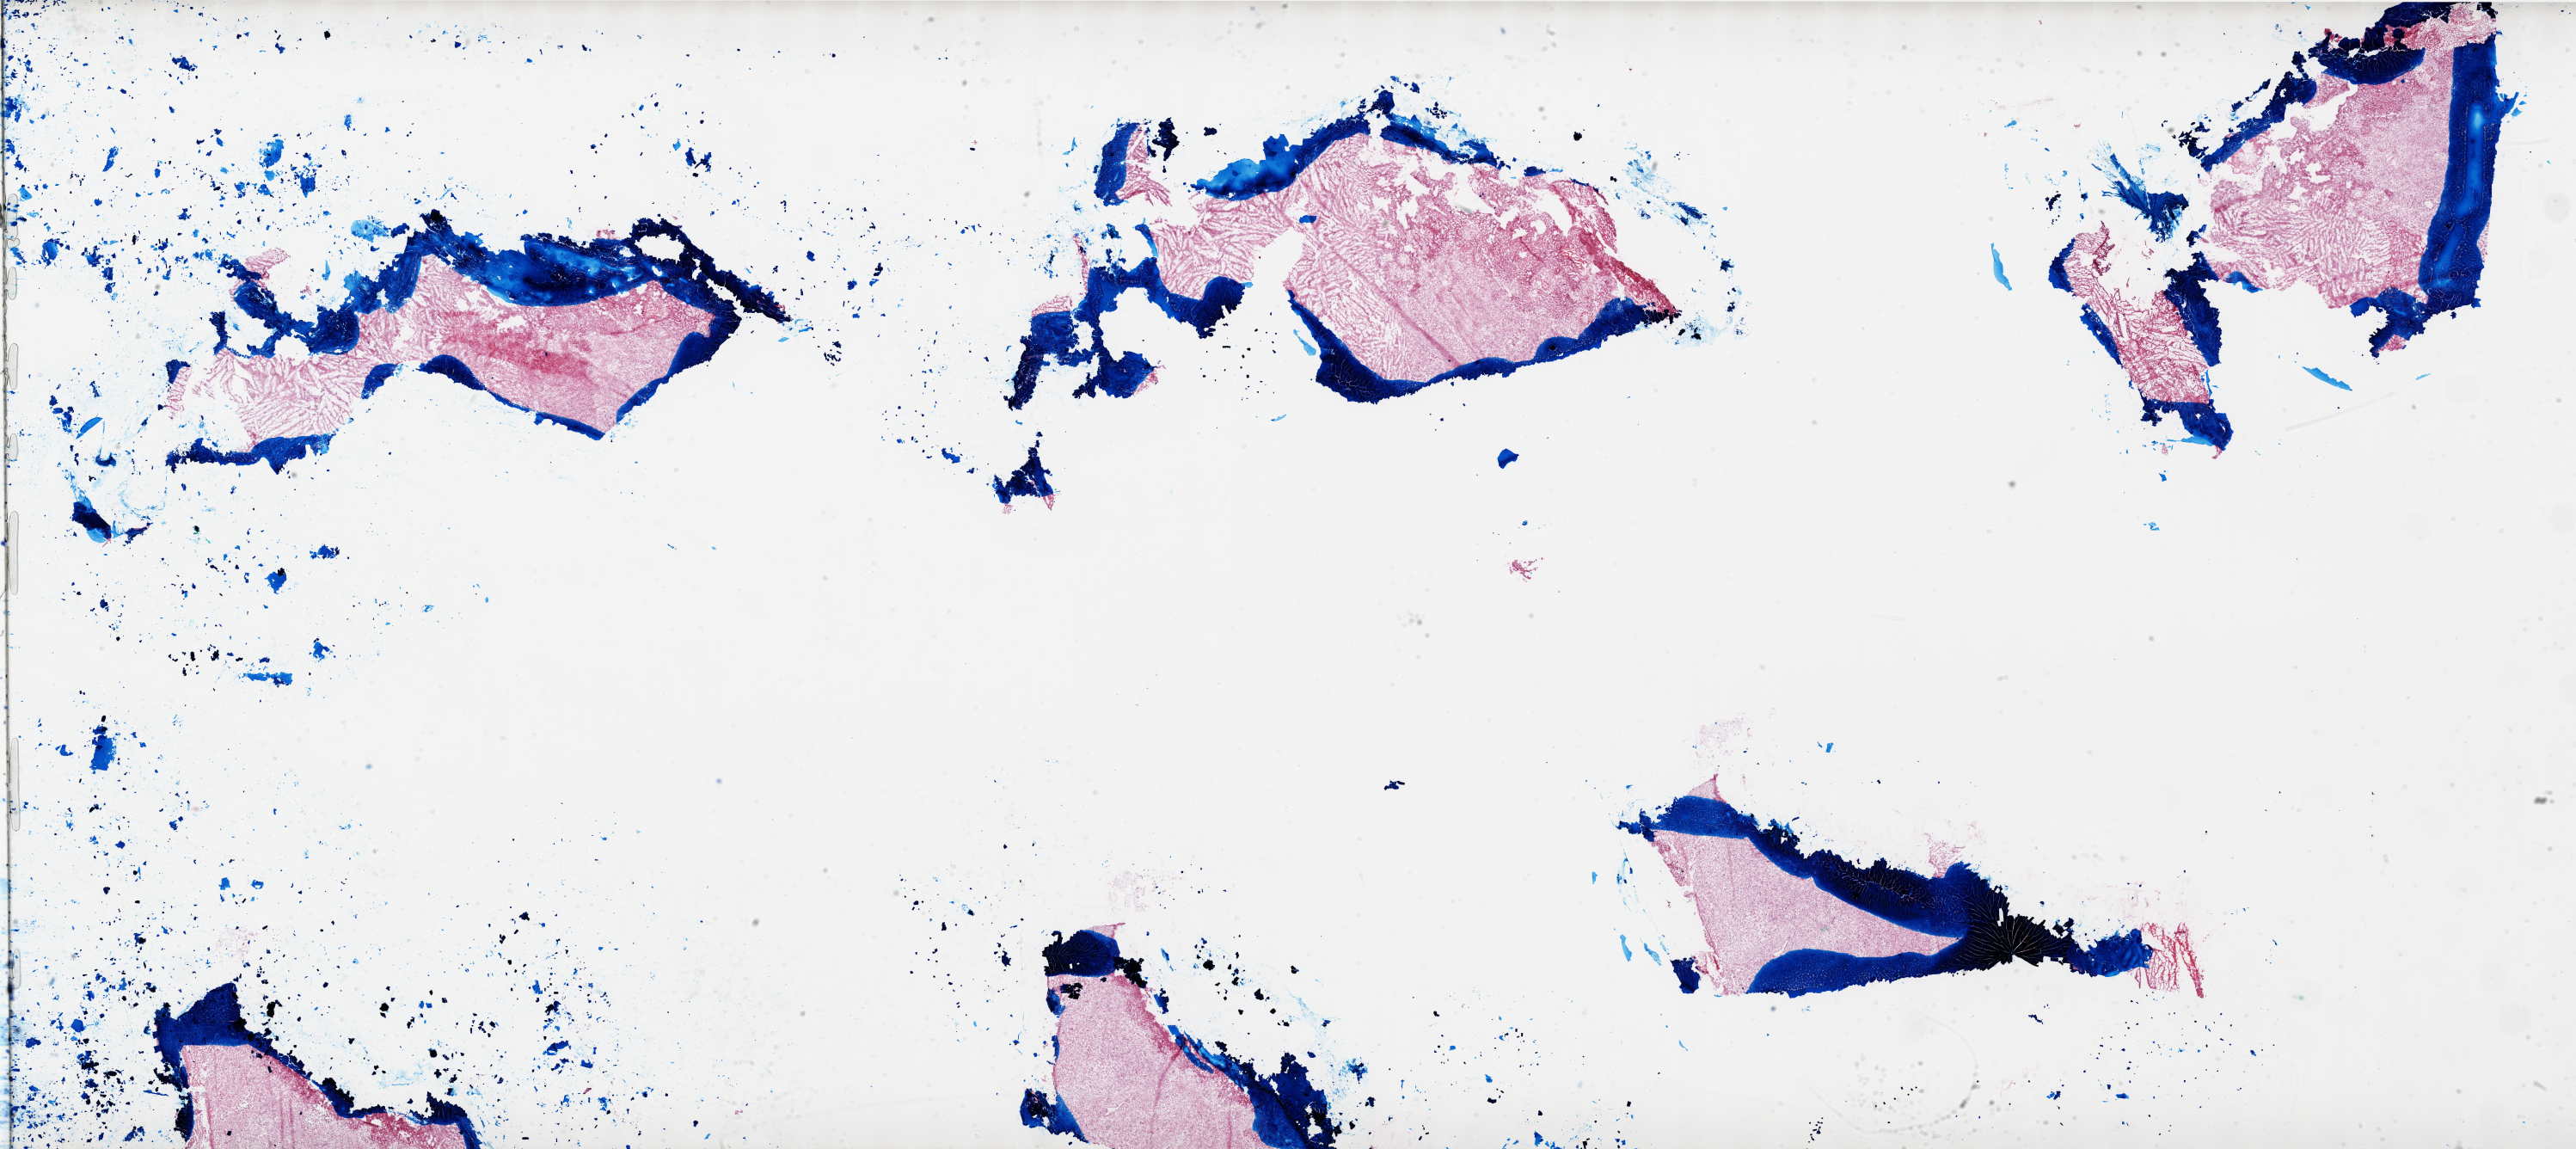
Whole-slide histology image, H&E — whole scanned area (about 48.0 x 21.4 mm, acquisition: 20x scan) shown as a low-resolution overview, frozen section, primary tumour sample from the brain. Female patient; age at initial diagnosis 56 years. Slide review estimates, as recorded: tumour cells 95%, tumour nuclei 100%, normal cells 0%, stromal cells 0%, necrosis 5%.
Diagnosis: Glioblastoma.